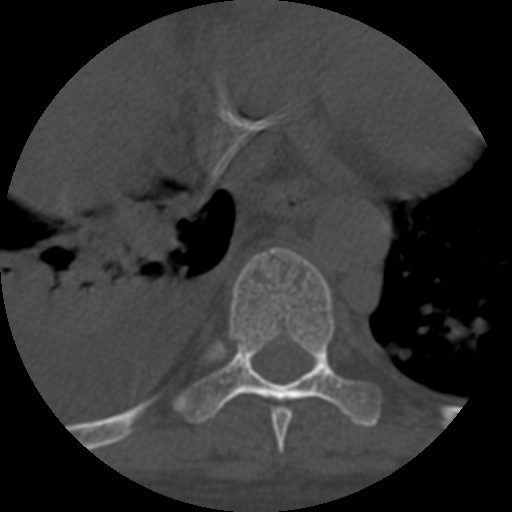
CT including the spine, one axial slice; slice 380 of 708 in the series (ordered by position); reconstruction kernel STANDARD; 120 kVp; one of 3 acquisitions stored at this slice position; bone window (W 1800 / L 400 HU); 1.25 mm slice thickness; 512 × 512 image matrix, field of view 160 × 160 mm. Patient age 55 years. From the clinical record (not read from this slice): primary cancer: colon; vertebrae with lytic lesions (as recorded): T12, L1, L5.
Structures marked on this image (semi-automatic segmentation, software-assisted and operator-edited):
- T8 vertebra: bounding box [x1, y1, x2, y2] px = [271, 407, 293, 453]
- T9 vertebra: [172, 247, 381, 428]